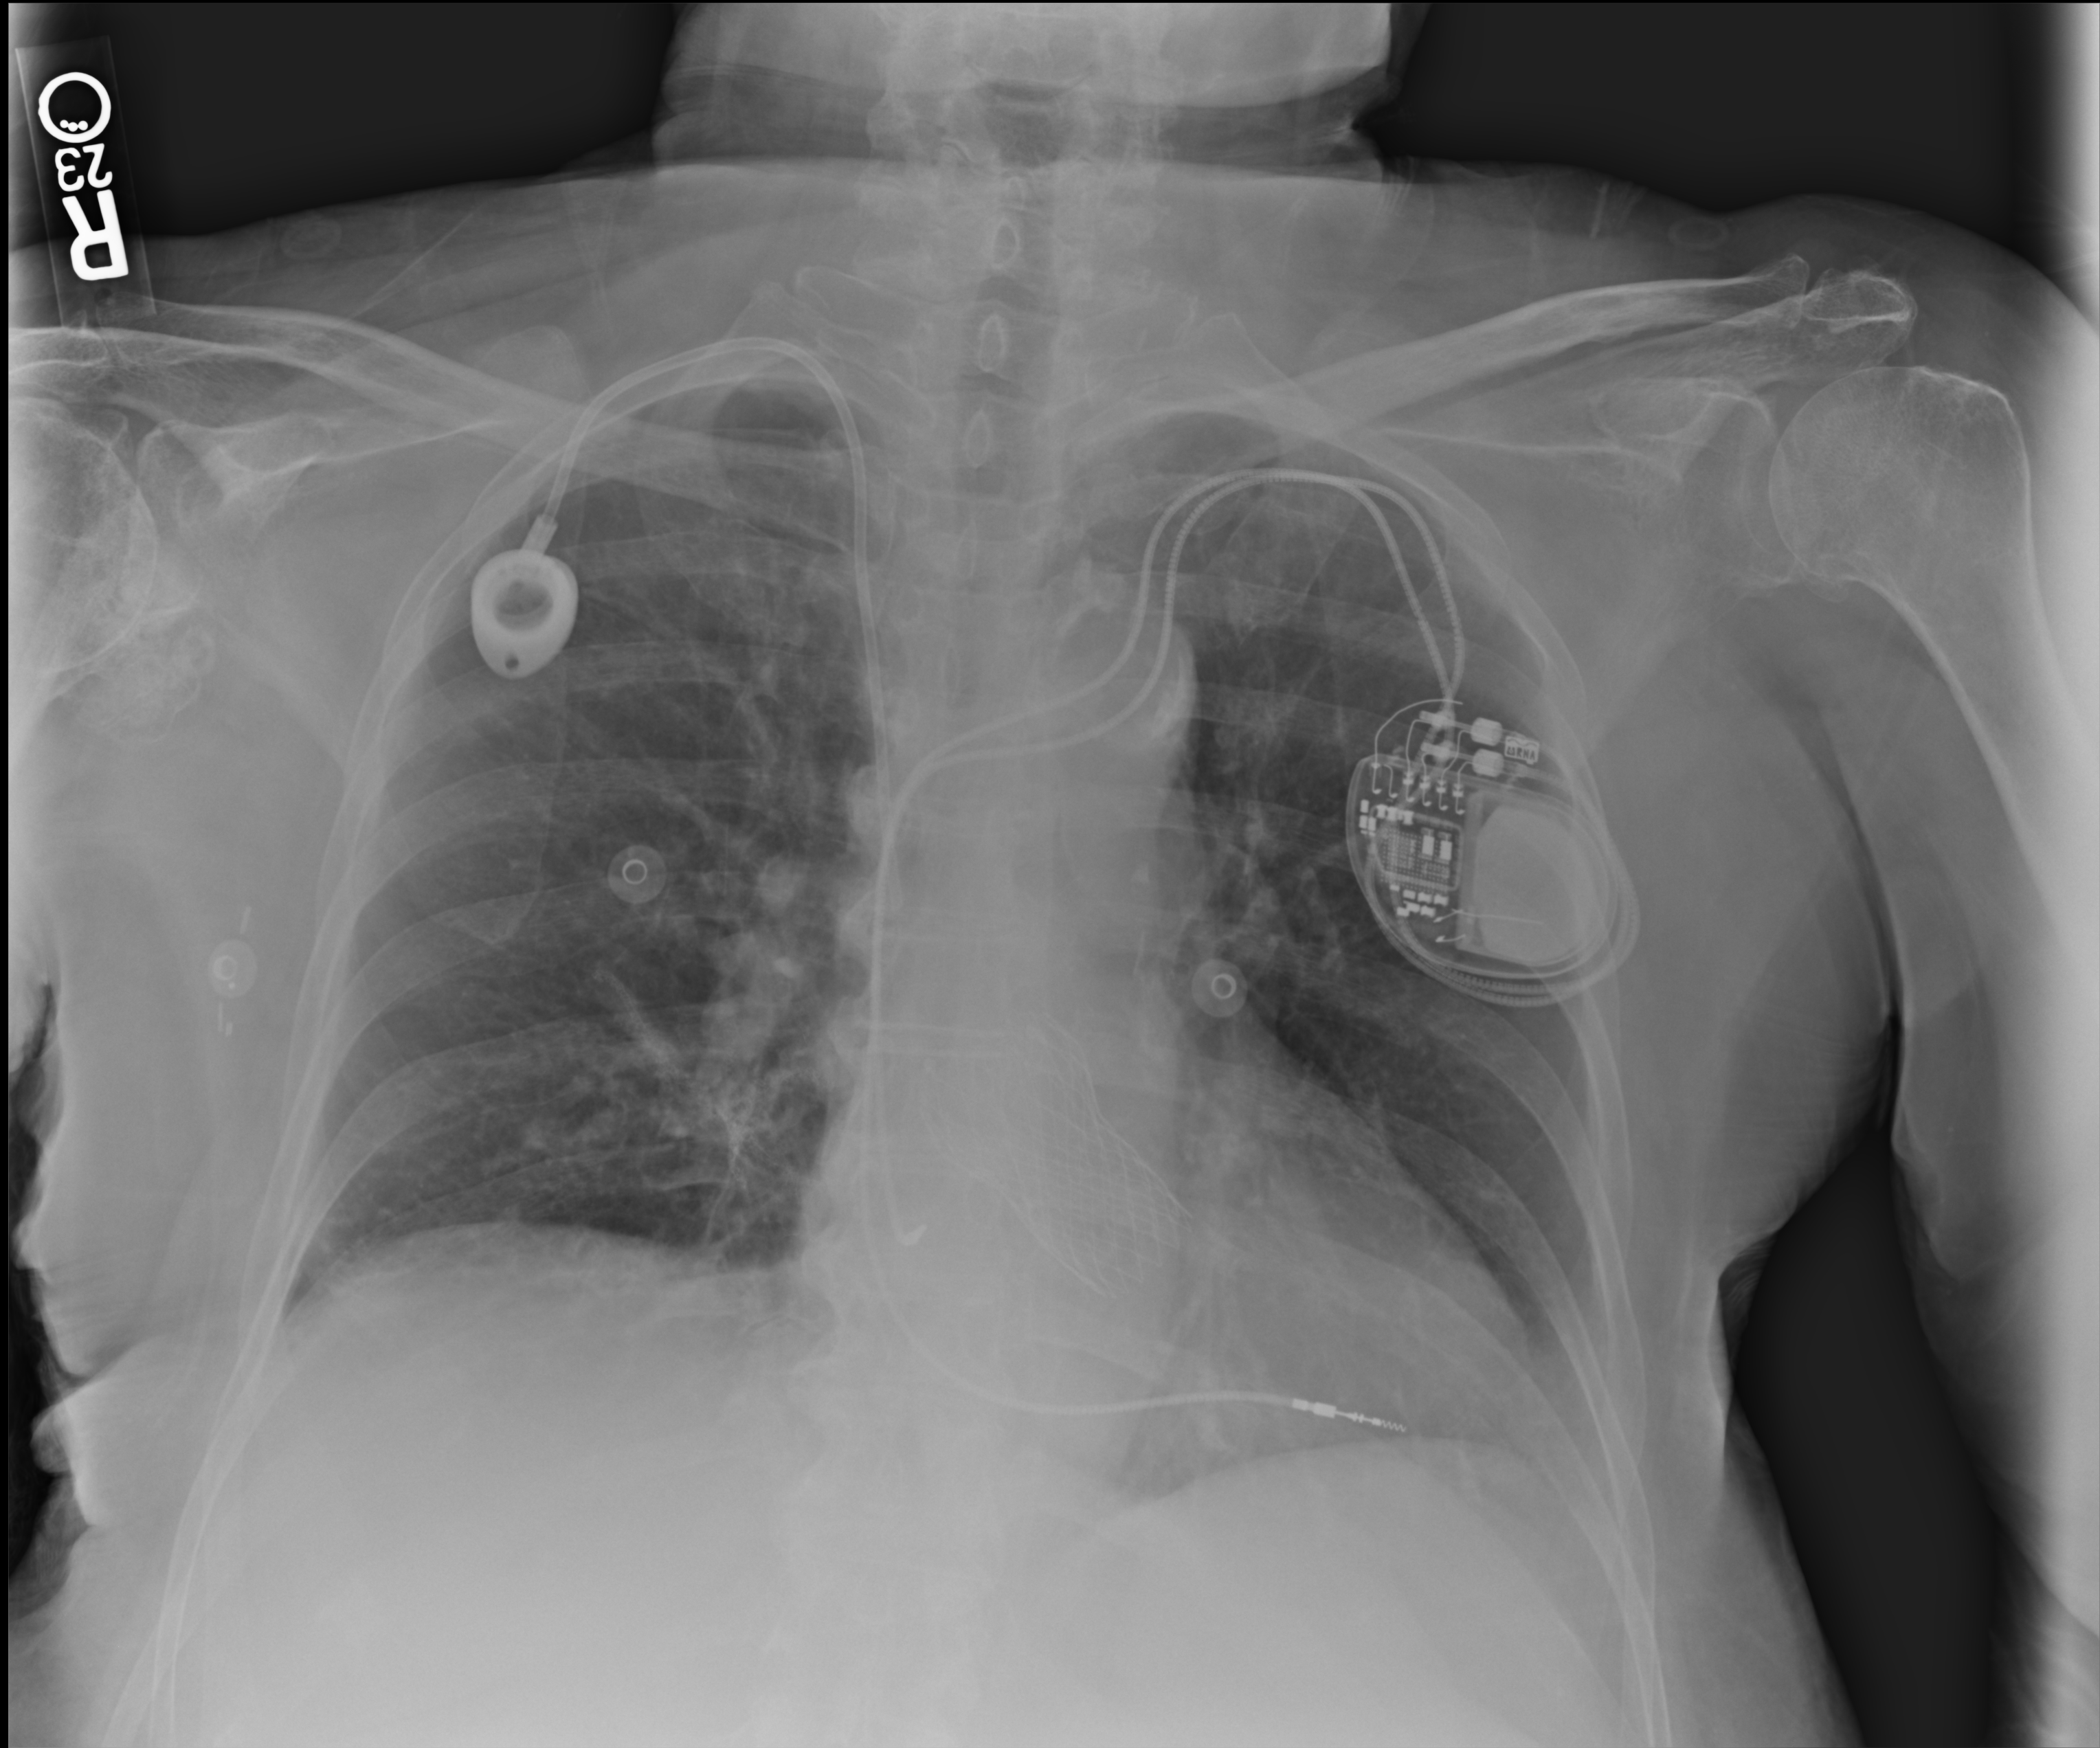
Chest X-ray (portable); anteroposterior (AP) projection. Patient hospitalised with COVID-19; female, aged 75–90 years.
From the hospital-stay record, not from the radiograph (when in the stay this image was taken is not recorded): mechanically ventilated during this hospital stay: no; admitted to intensive care during this hospital stay: no.